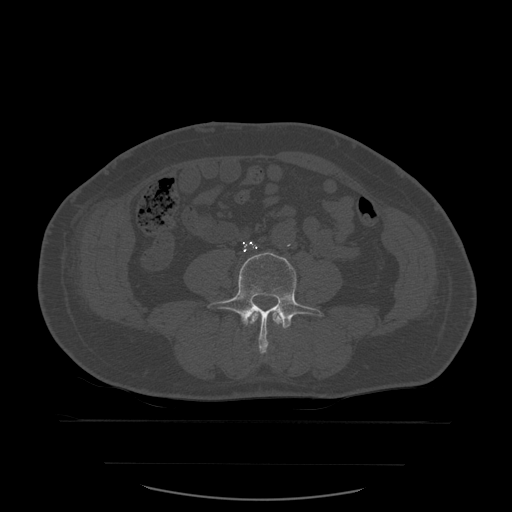
CT including the spine, one axial slice. Position 170 of 590 along the scan axis. Bone window (W 1800 / L 400 HU). 1.25 mm slice thickness. 512 × 512 image matrix, field of view 479 × 479 mm. Patient age 71 years. Case-level facts recorded for this patient, not image findings: primary cancer: lung.
Annotated regions visible in this slice (semi-automatically segmented with operator editing):
- L3 vertebra: bounding box [x1, y1, x2, y2] px = [249, 312, 285, 353]
- L4 vertebra: [208, 252, 322, 354]